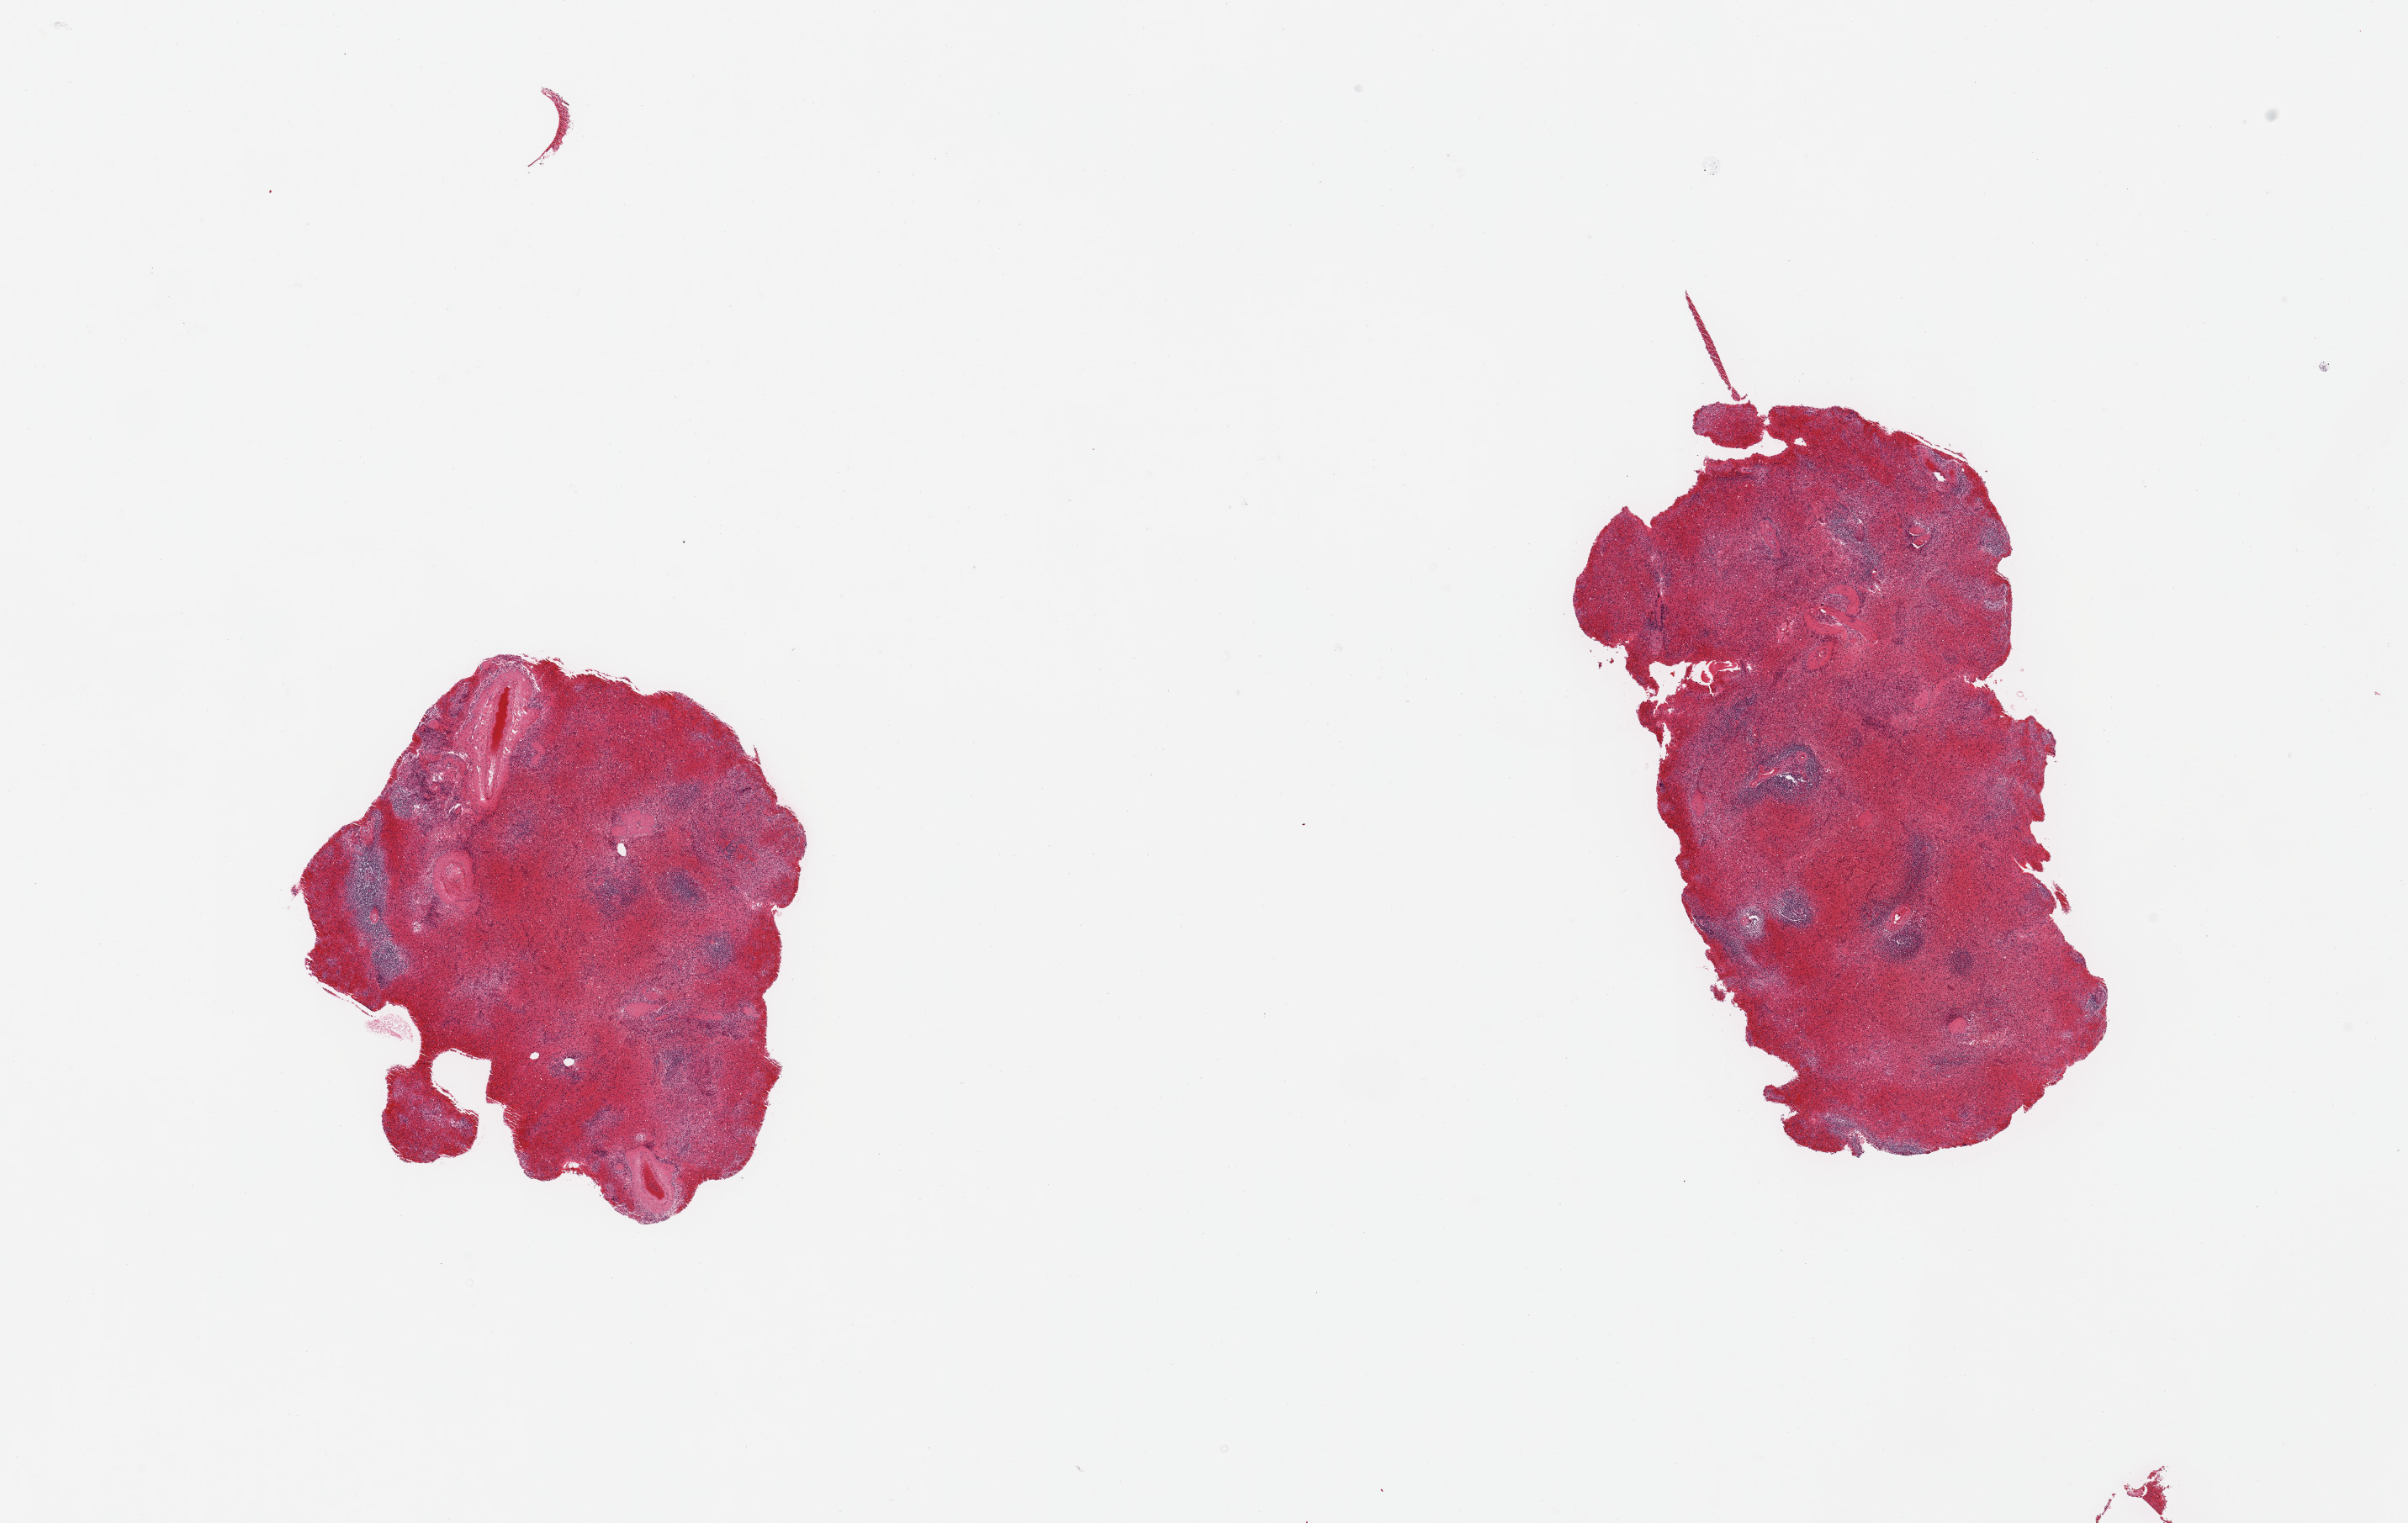
Hematoxylin and eosin (H&E) whole-slide image, brightfield, a low-resolution overview of the entire scanned area, about 22.6 x 14.3 mm. PAXgene-fixed, paraffin-embedded tissue. Target tissue: spleen. Donor tissue sample. Donor sex: male.
Pathologist's review note for this sample: 2 pieces; moderately congested; prominent white pulp.